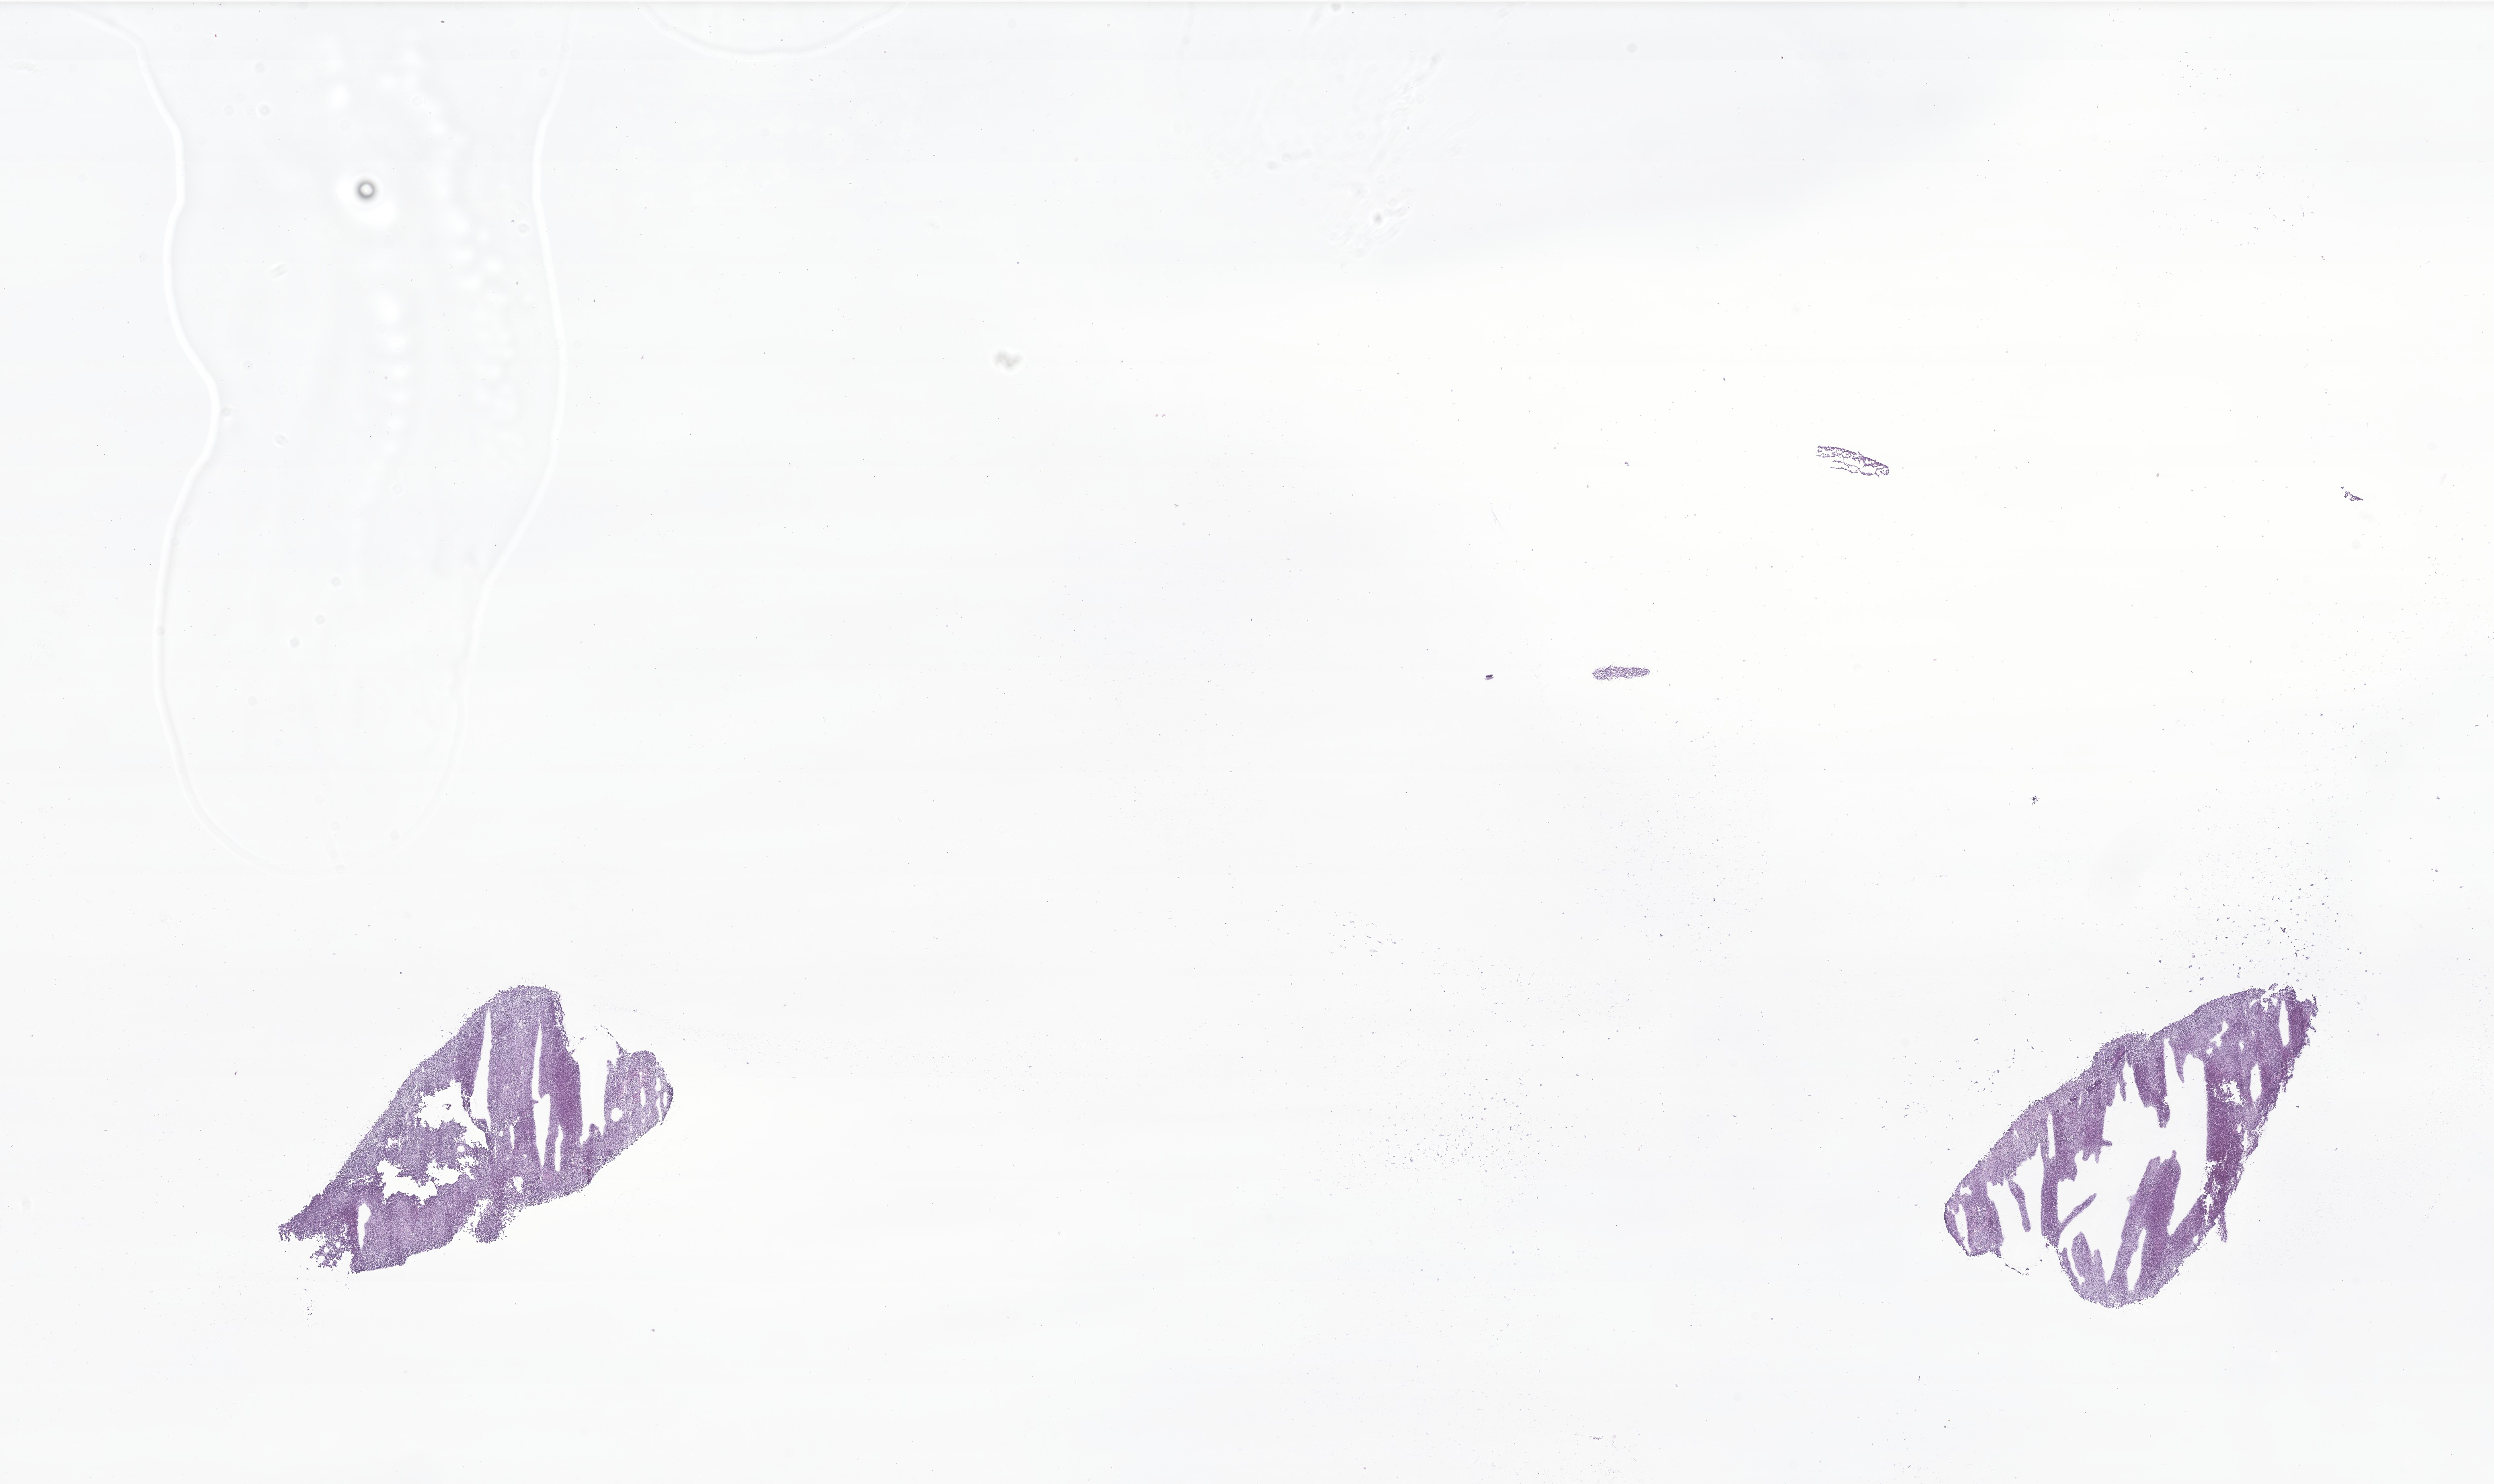
Whole-slide image, haematoxylin and eosin stain of tumor tissue from the brain — a low-resolution overview of the entire scanned area, about 26.2 x 15.6 mm. Cryosection (OCT / tissue freezing medium). Patient: male, age 54 months (4 years 6 months).
- diagnosis: Medulloblastoma, NOS